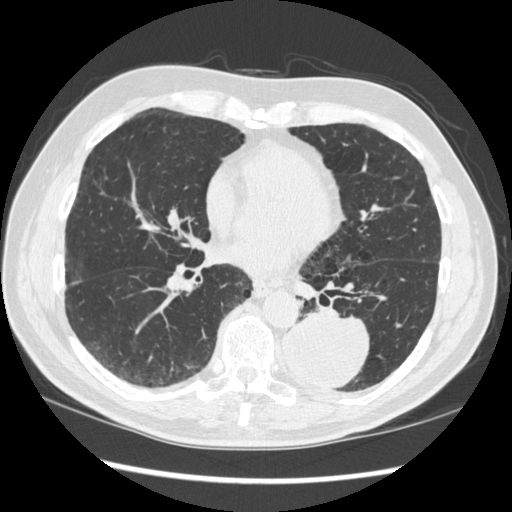
Low-dose screening chest CT, axial slice; first (baseline) screen; lung window (W 1500 / L -600 HU); 1.25 mm slice thickness; 120 kVp; slice 145 of 348 in the series. Male participant, aged 72 years at enrolment. Current smoker at enrolment.
Lesion marked by an expert reader, bounding box (x1, y1, x2, y2) in pixels: (268, 302, 372, 393). The screening reader recorded 2 non-calcified nodules or masses ≥4 mm on this exam (left lower lobe, right middle lobe); which of them this box marks is not recorded. Participant outcome: lung cancer diagnosed 37 days after this screen — squamous cell carcinoma, NOS, left lower lobe, stage IIIA (AJCC 6th edition), 60 mm at pathology.